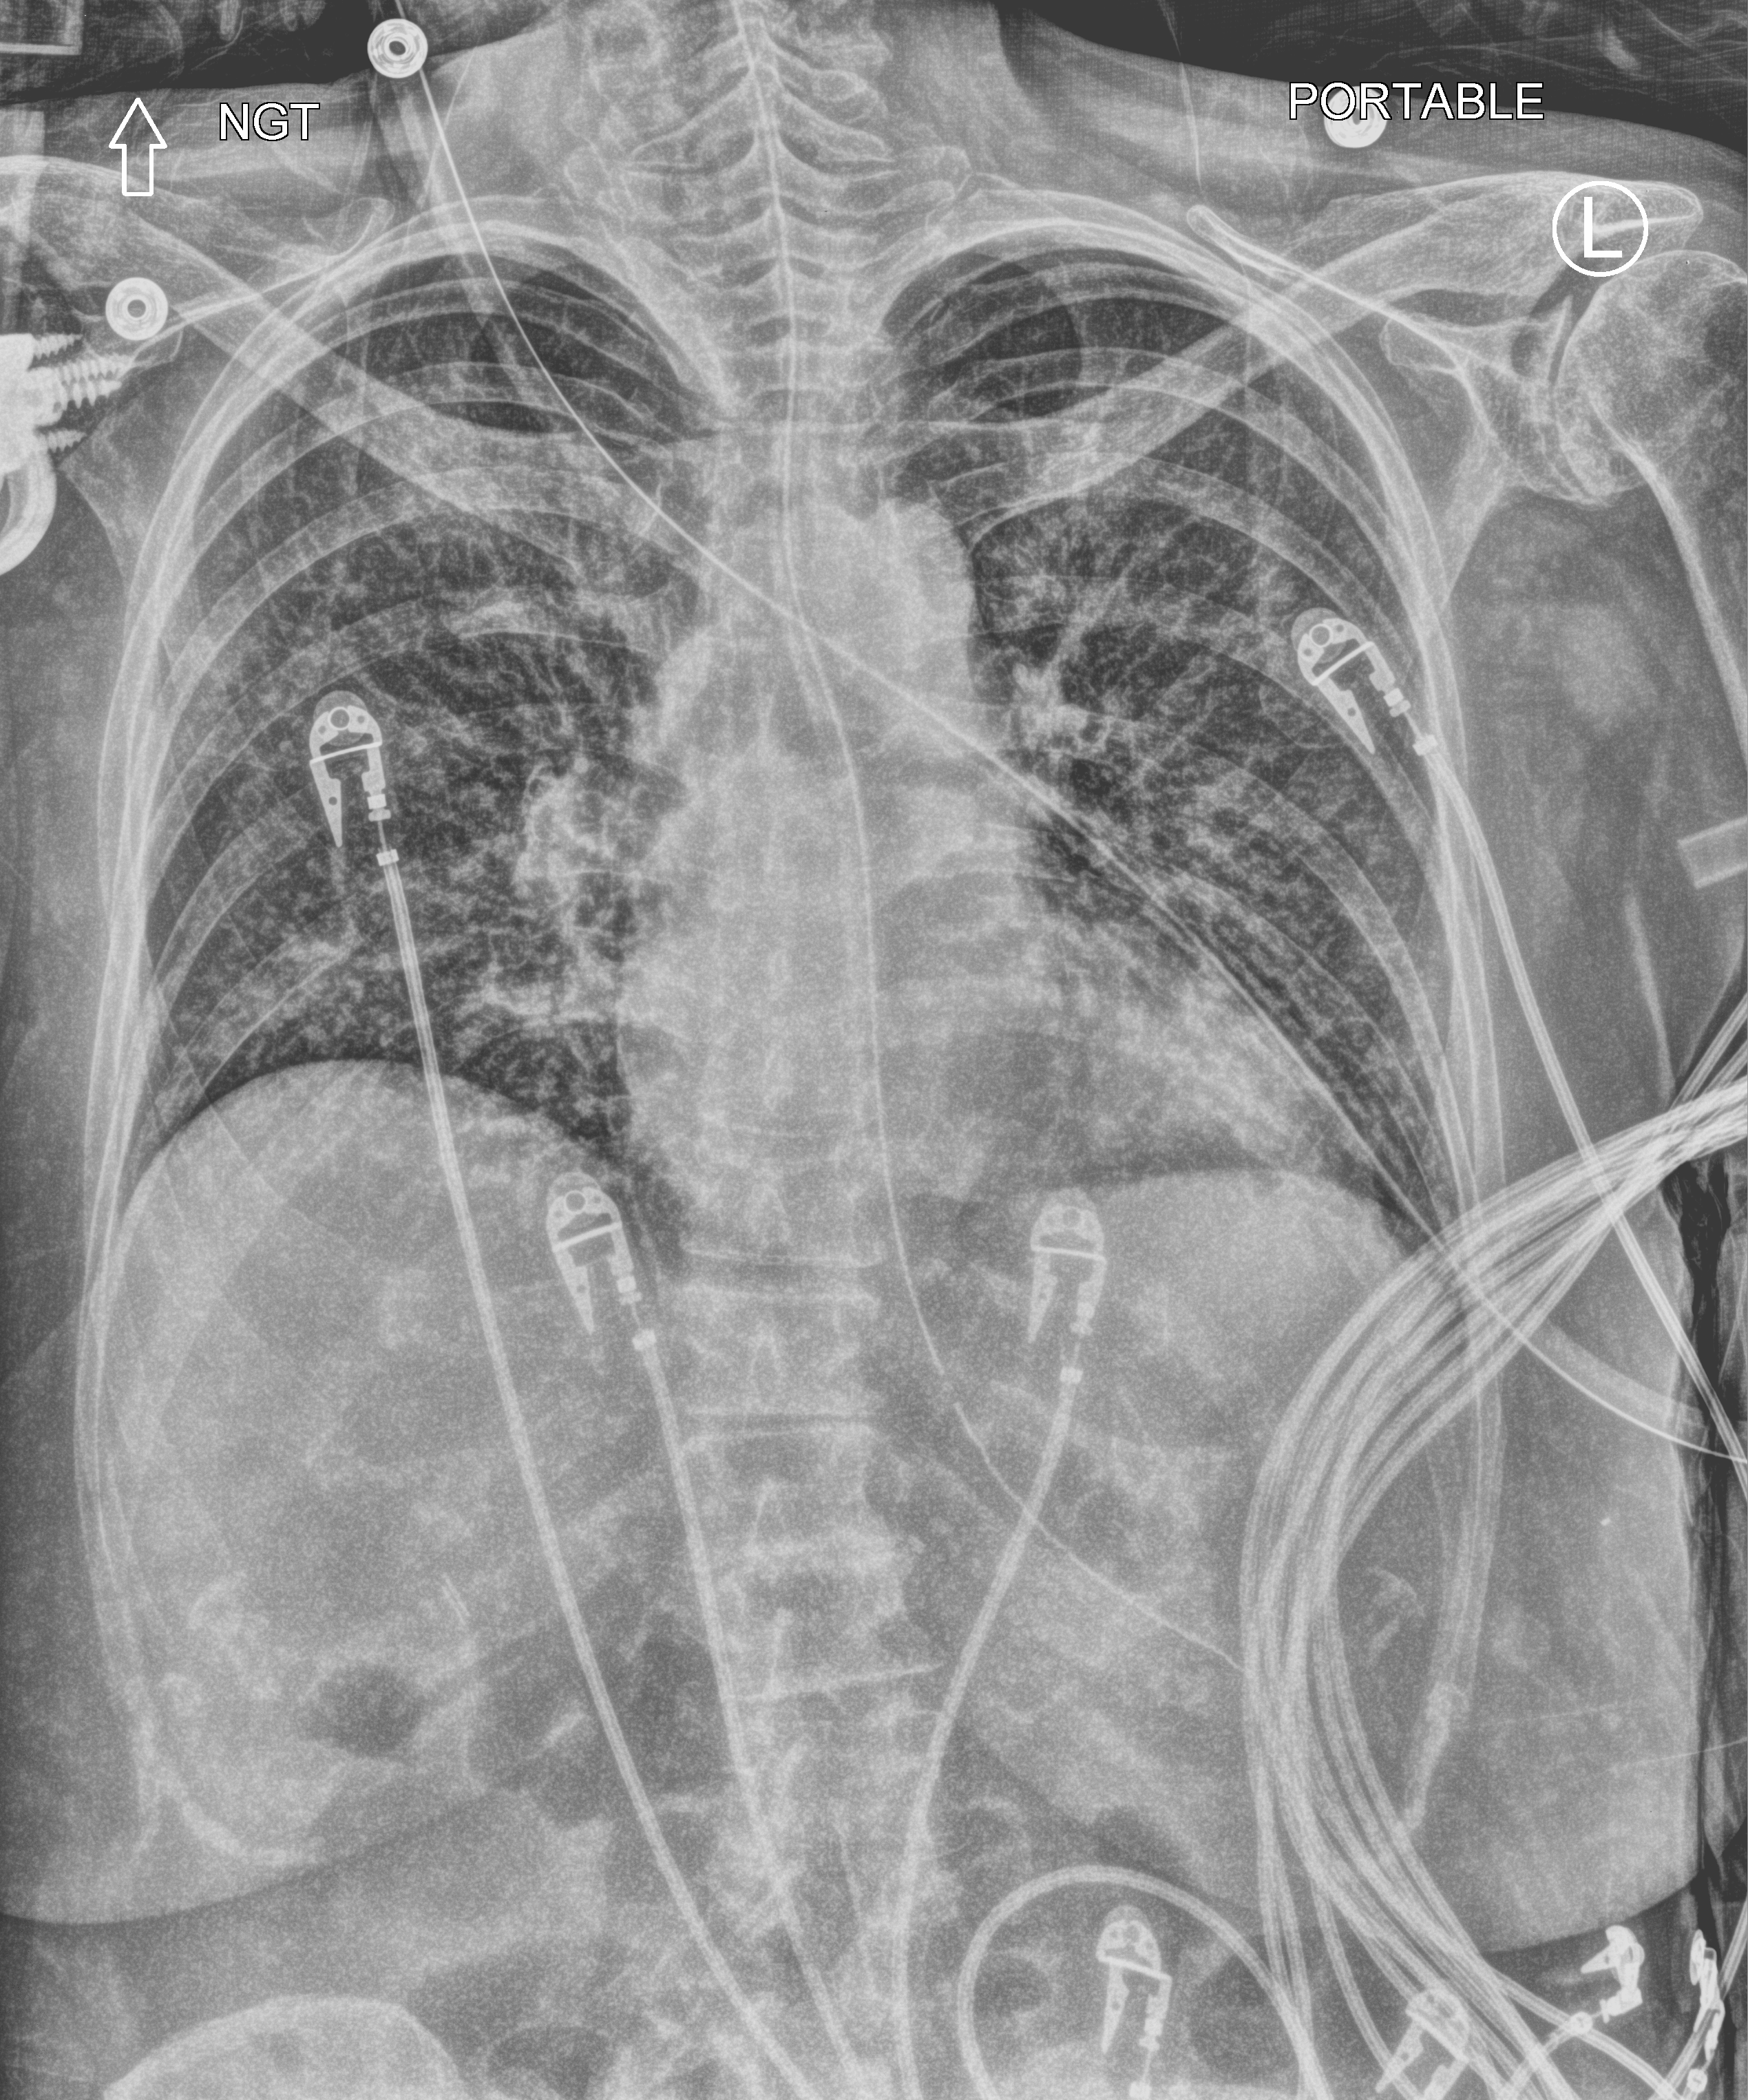
Bedside chest radiograph (computed radiography), anteroposterior (AP) projection. Female patient hospitalised with COVID-19, age 60–74 years.
Hospital-stay facts (about this admission, not read from this image; timing relative to this image not recorded): mechanically ventilated during this hospital stay: yes.